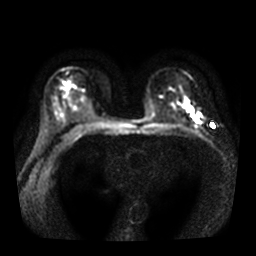
Breast MRI, one axial slice. Position 21 of 36 along the scan axis. Diffusion-weighted series; image 2 of 4 stored at this slice position (different b-values; order by instance number). 3 T. 5 mm slice thickness. 256 × 256 image matrix. Female patient.
Outlined on this slice (manually delineated by an expert):
- tumour on diffusion-weighted imaging: bounding box <186,107,200,122> (left, top, right, bottom; pixels)